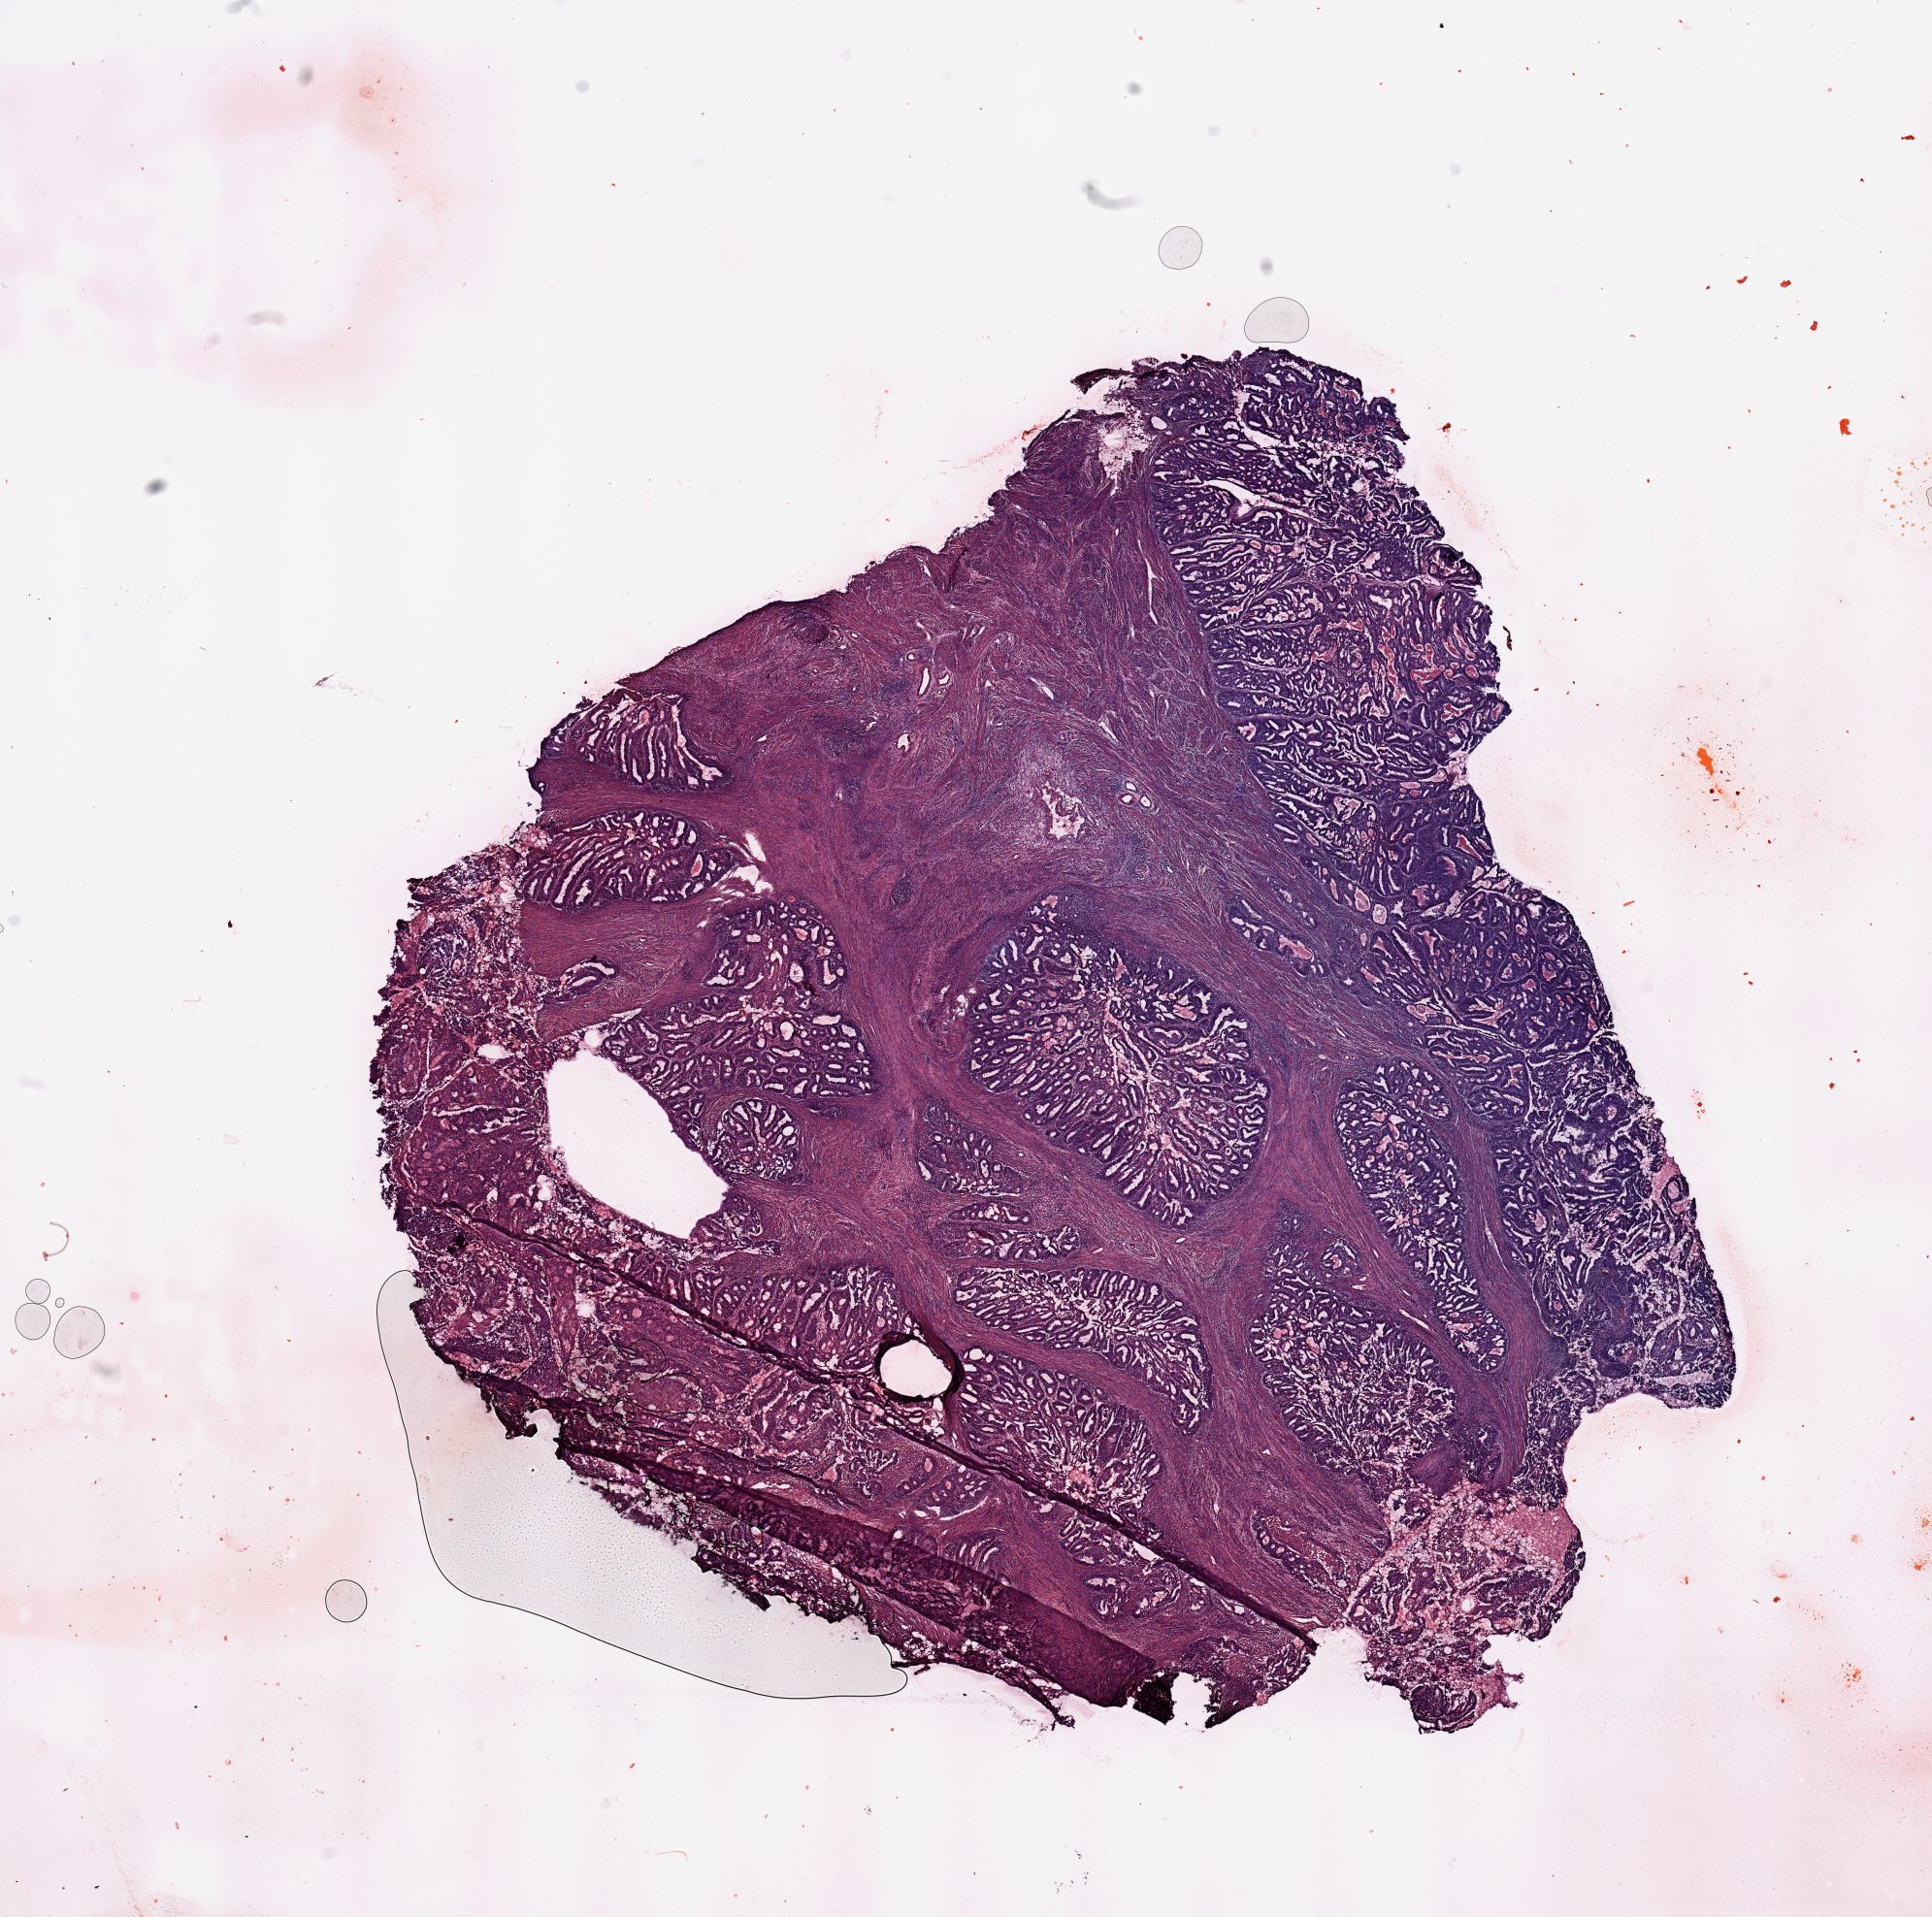
H&E-stained whole-slide image, whole scanned area (about 15.8 x 15.6 mm, acquisition: 20x scan) shown as a low-resolution overview, tumour tissue sample, sampled site: uterus. 66-year-old female patient. Pathologist review of this section (percent, as recorded): tumour nuclei 80%, necrosis 0%.
Histologic diagnosis: Endometrioid adenocarcinoma, NOS.